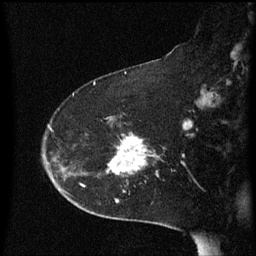
Breast MRI (dynamic contrast-enhanced), one sagittal slice; position 40 of 60 along the scan axis; dynamic contrast-enhanced series, image 2 of 3 at this slice position (ordered by acquisition); 1.5 T; TE 4.2 ms, TR 8.4 ms; 256 × 256 image matrix. Female patient, age 54 years. From the clinical record (not read from this slice): setting: breast cancer imaged before/during neoadjuvant chemotherapy; receptor status: HR-positive, HER2-negative.
Annotated regions visible in this slice (semi-automatic segmentation, software-assisted and operator-edited):
- analysis volume of interest (the breast-tissue region the enhancement analysis was run in; not a lesion): box from (x=95, y=120) to (x=160, y=179) px
- tumour enhancement mask (voxels above the 70 % enhancement threshold inside the analysis volume of interest): (x=111, y=136)–(x=148, y=175)